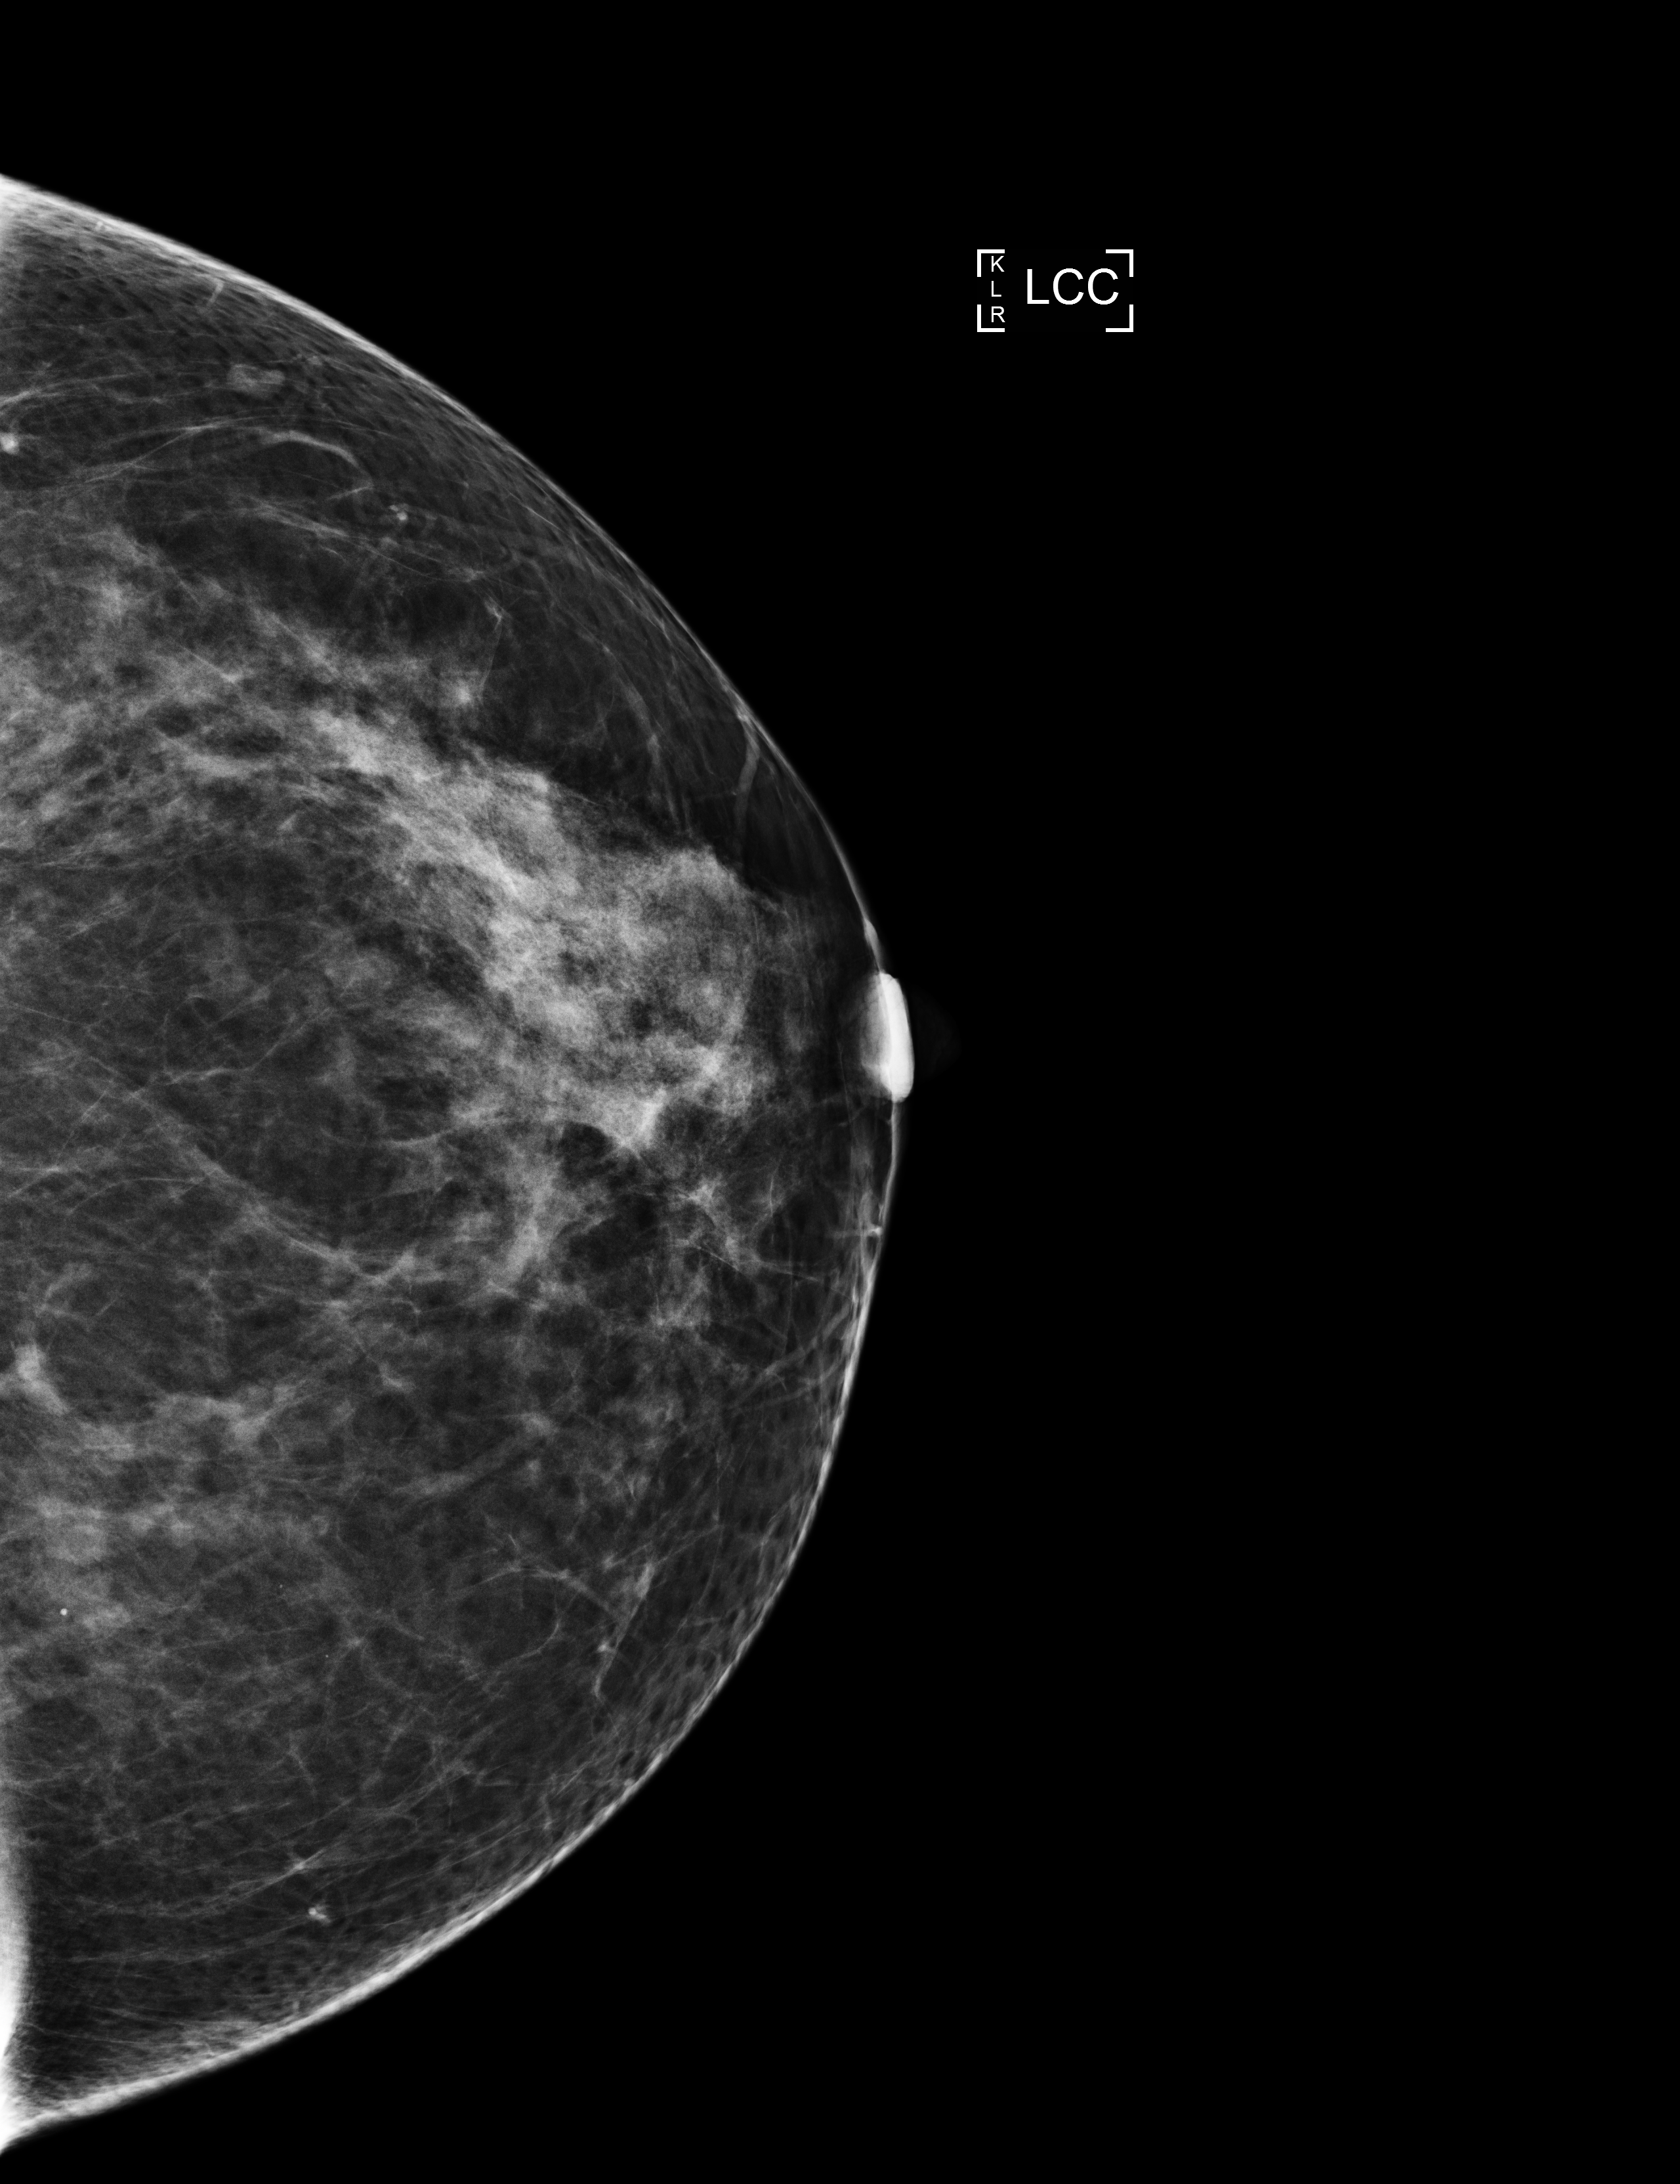
Annual screening mammography examination; compressed breast thickness 82 mm. Patient aged 51 years (female).
Image type: full-field digital mammogram. Breast: left. Projection: cranio-caudal projection.